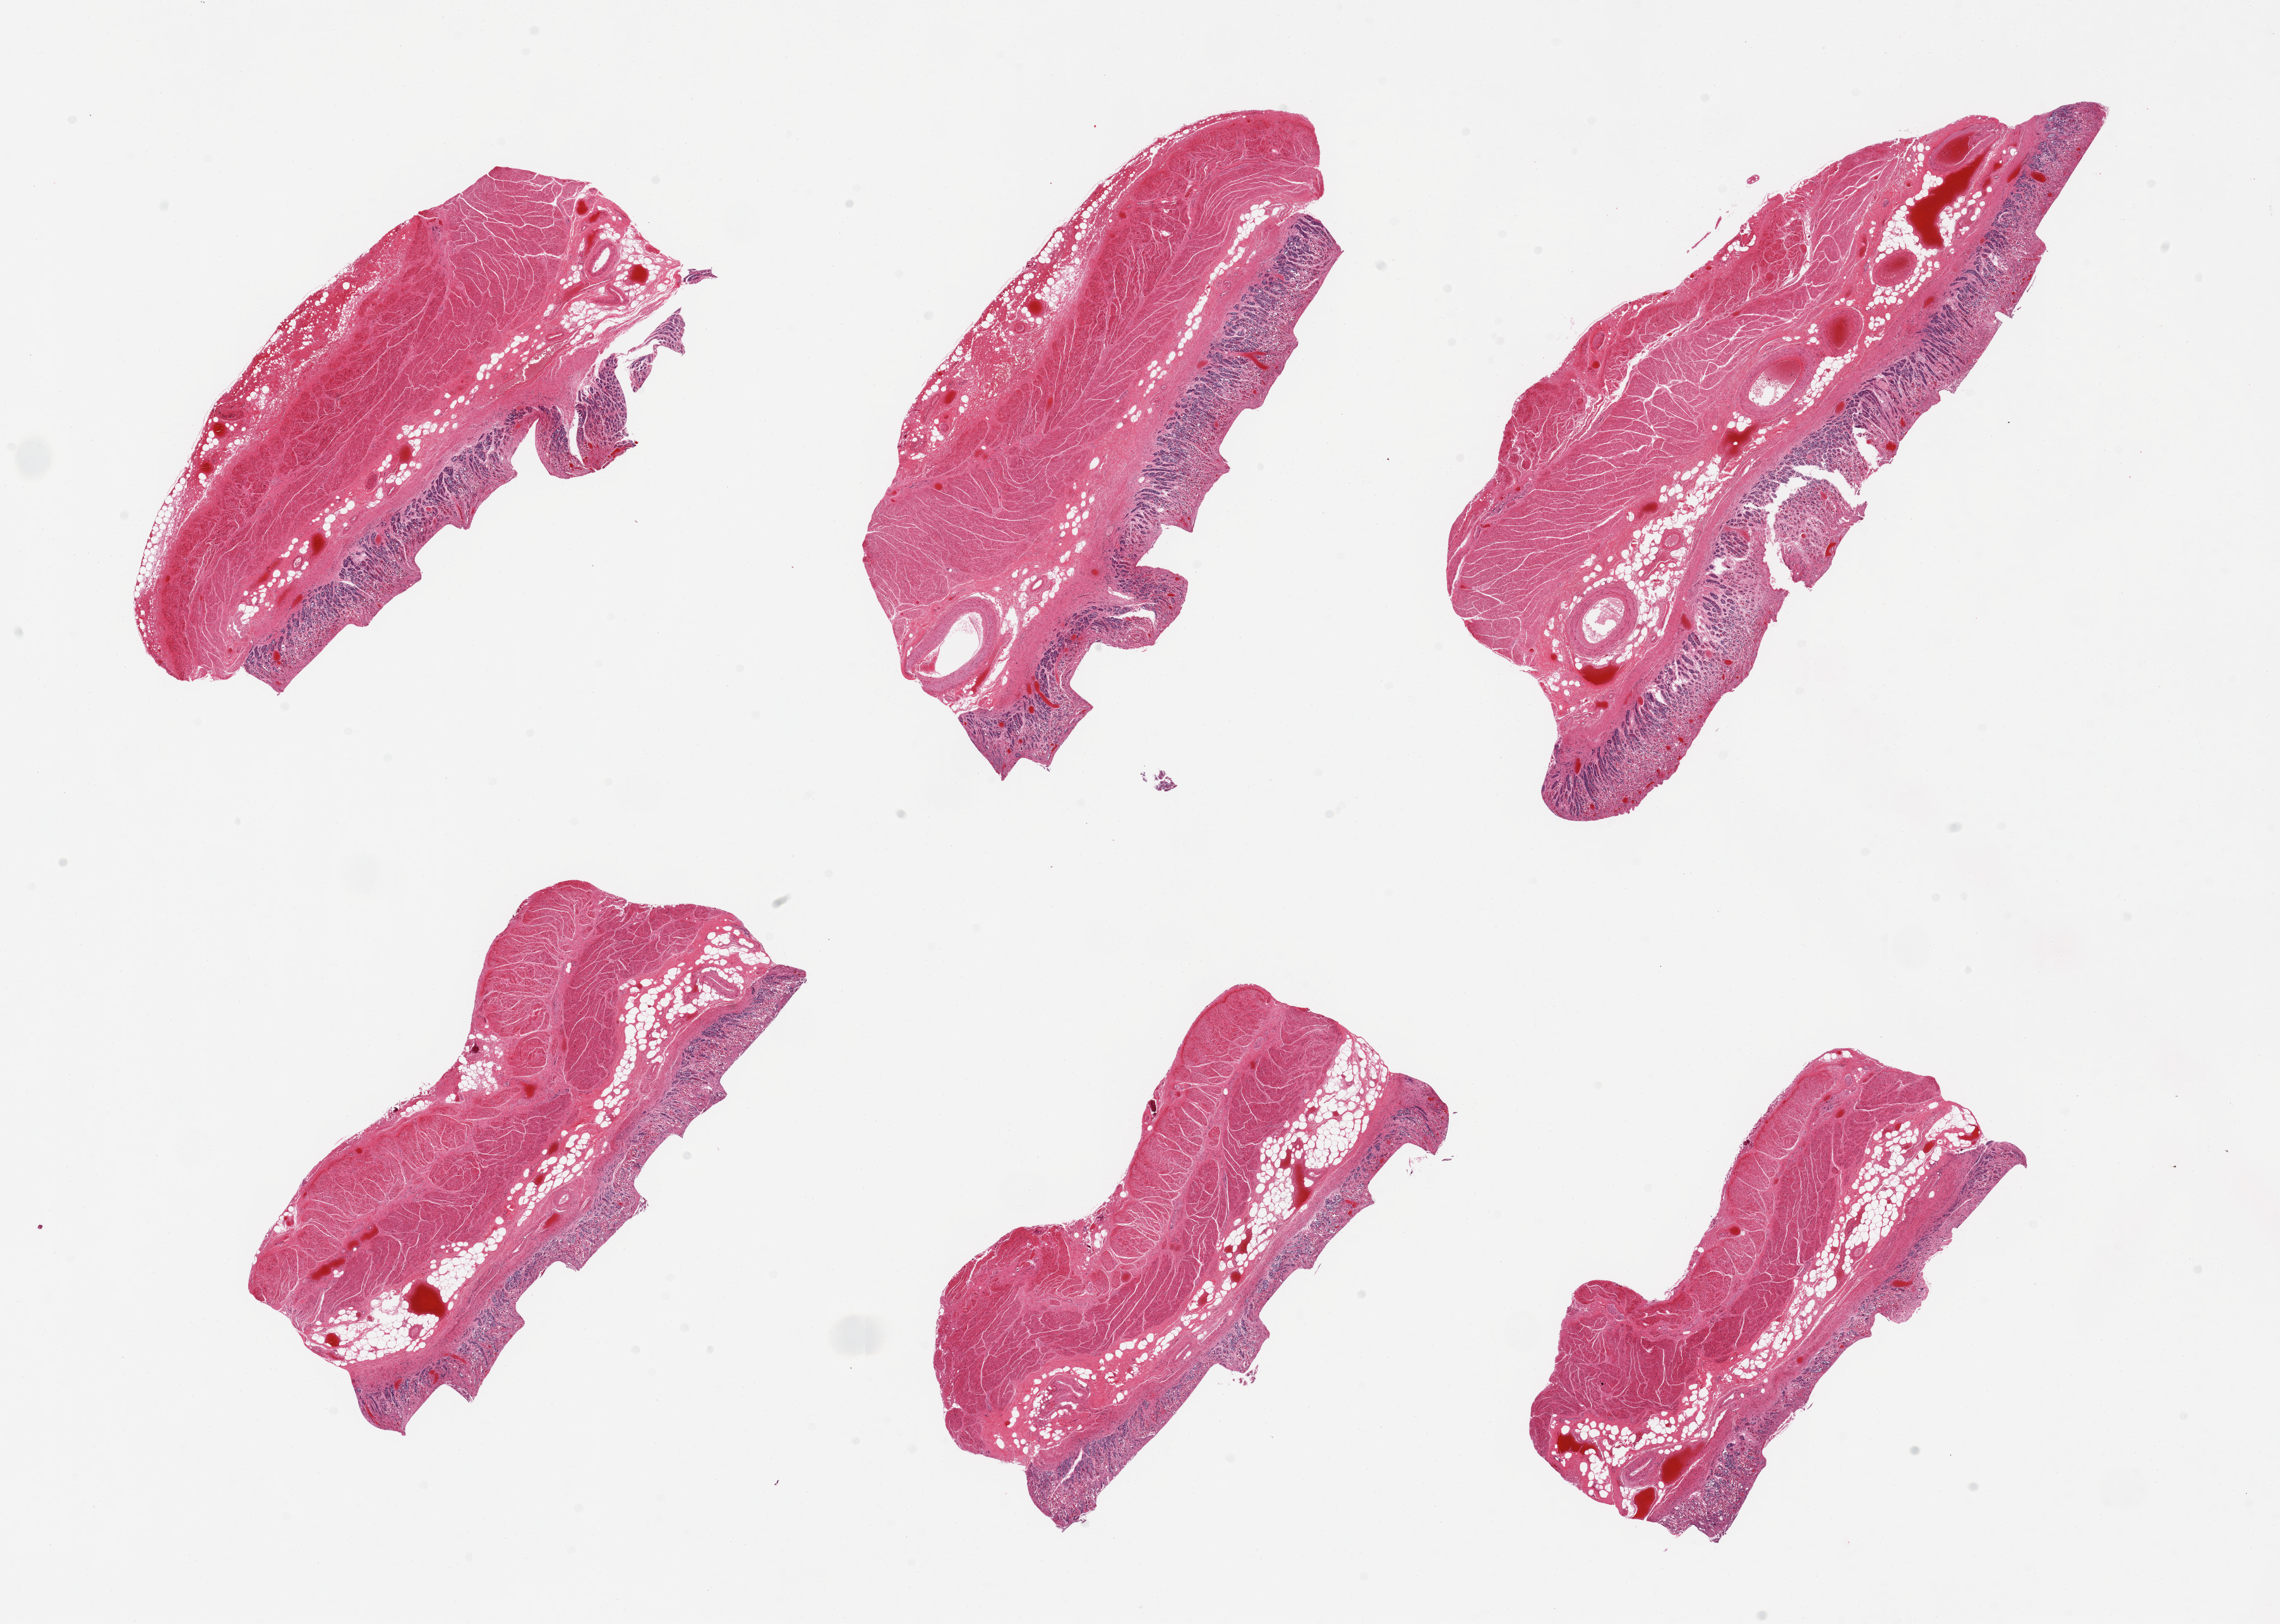
Hematoxylin and eosin (H&E) whole-slide image, brightfield, a low-resolution overview of the entire scanned area, about 28.5 x 20.3 mm (acquisition: 20x scan). PAXgene-fixed paraffin-embedded (PFPE) section. Section of gastroesophageal junction (target tissue). Donor tissue sample.
Review note (as recorded): 6 pieces, attached moderately autolyzed gastric mucosa, not correct target.